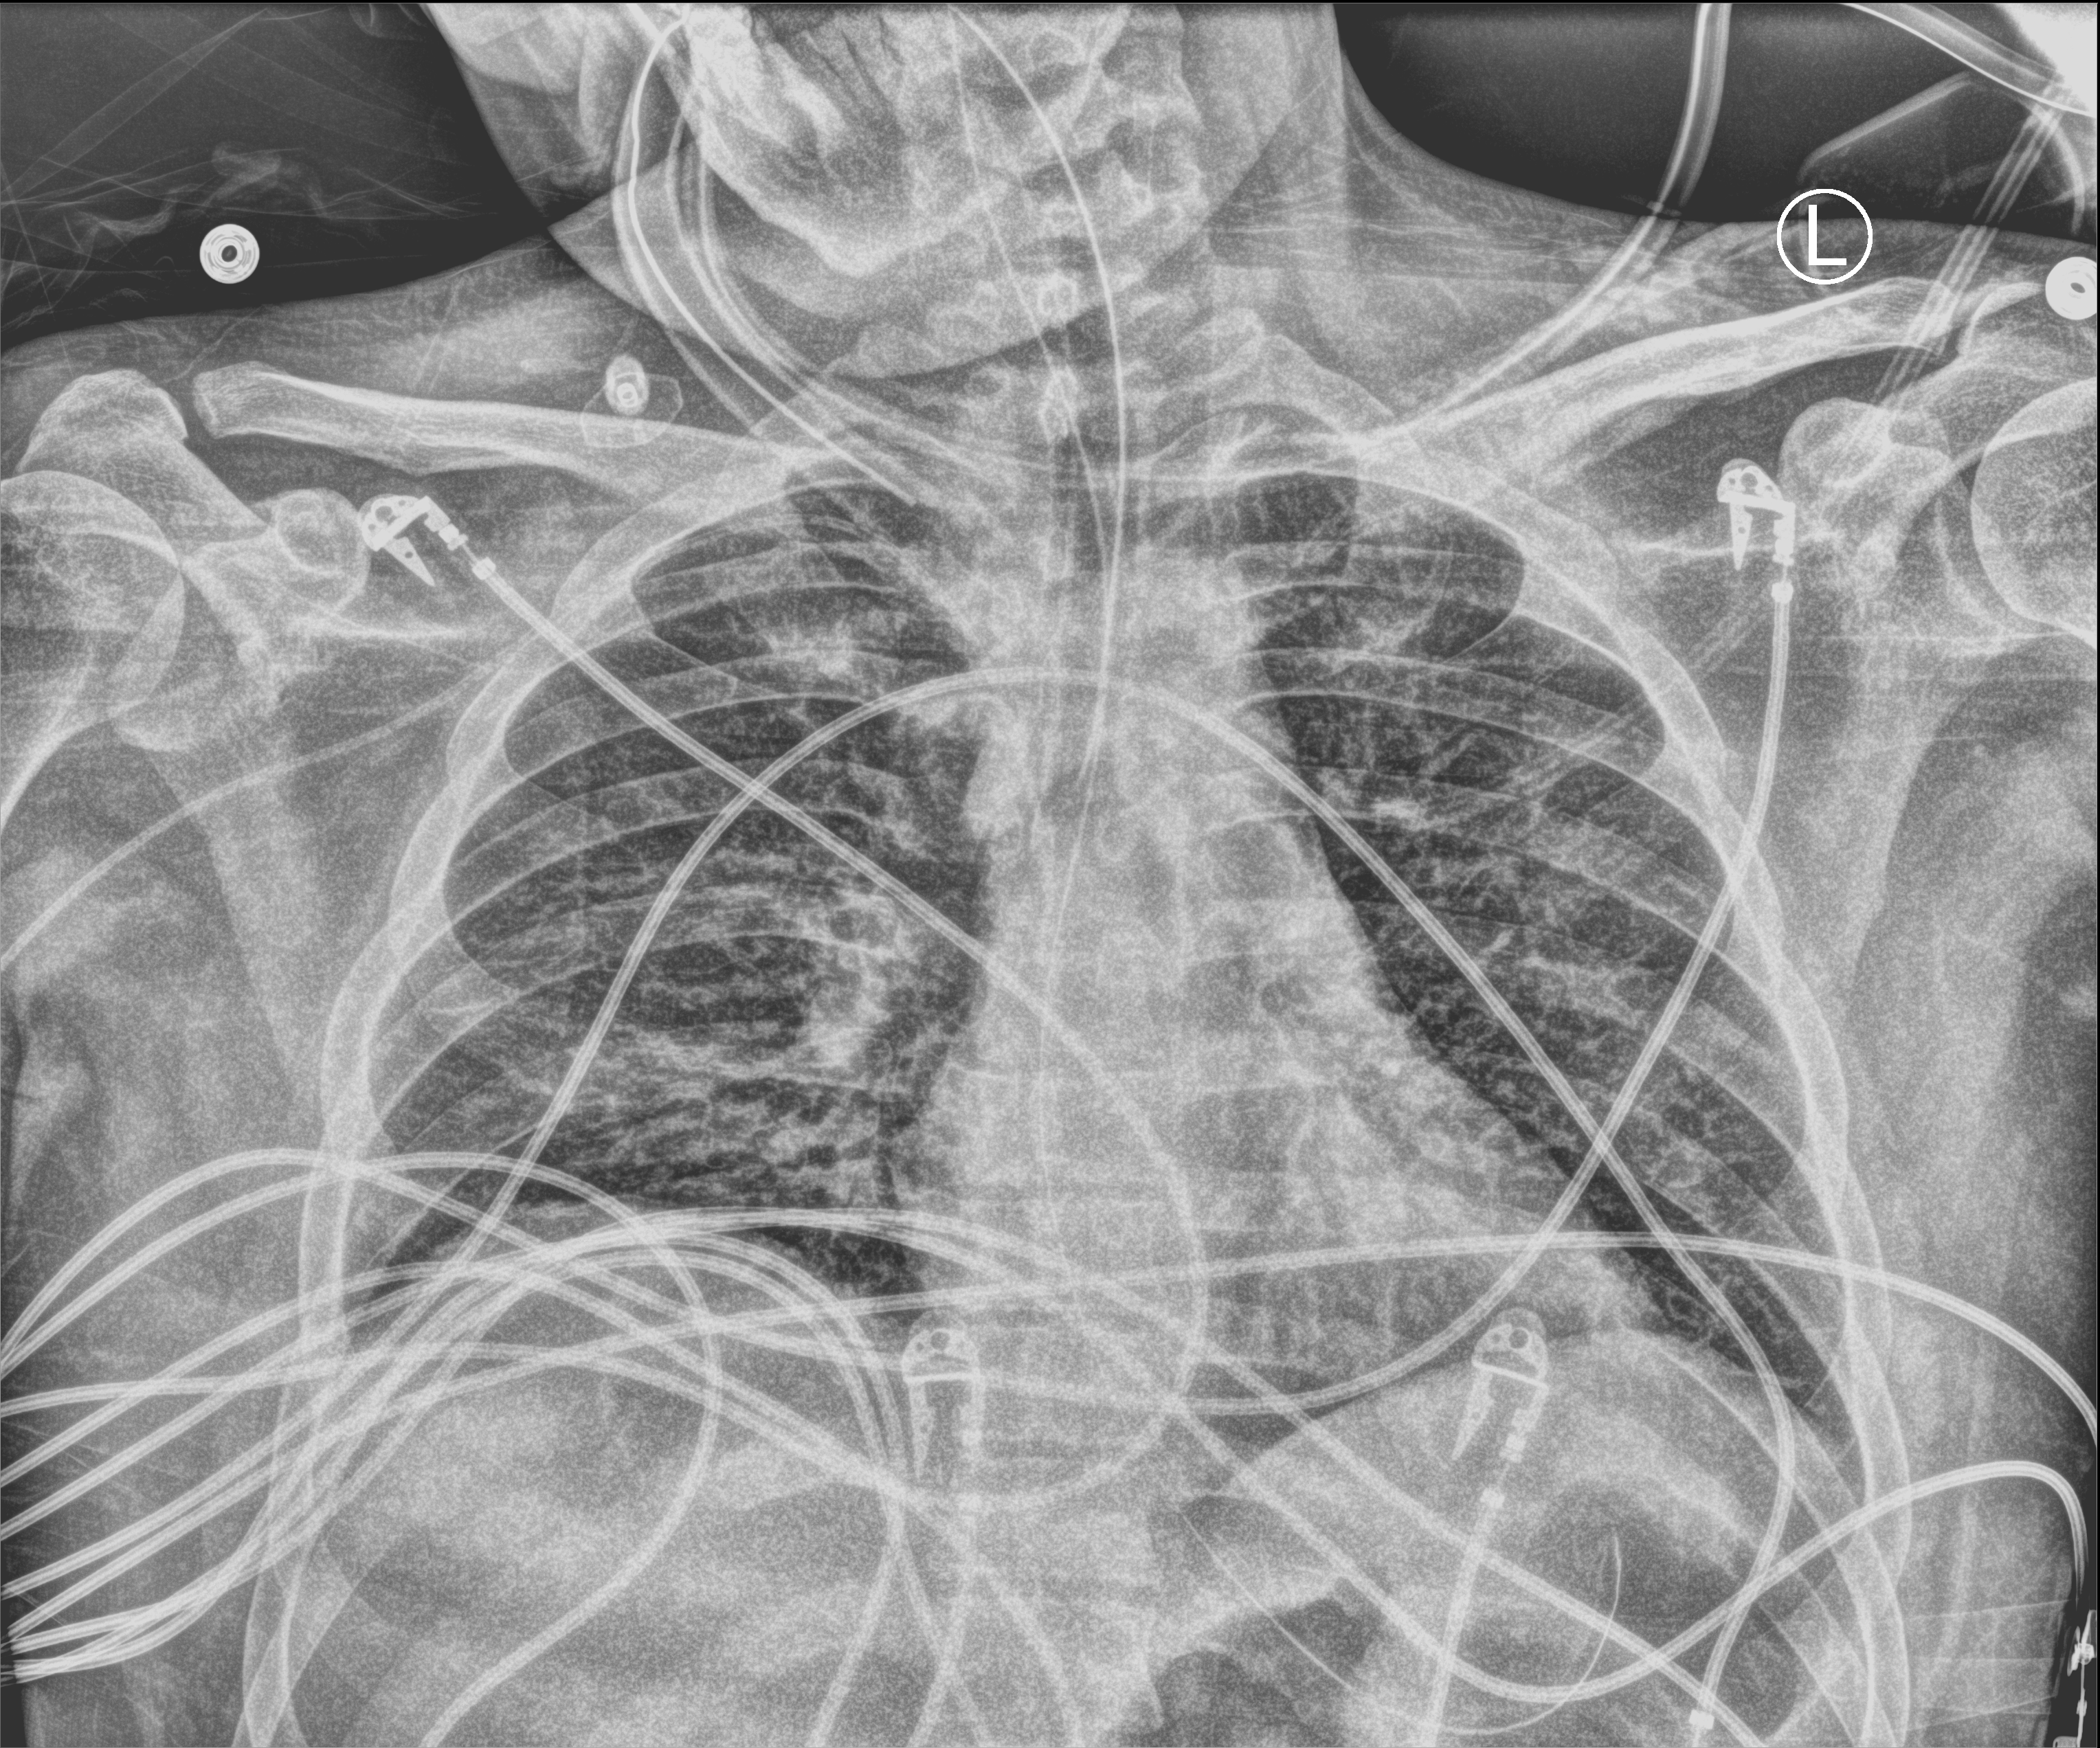
Chest X-ray (portable); anteroposterior (AP) projection. Patient hospitalised with COVID-19; male, aged 18–59 years.
Hospital-stay facts (about this admission, not read from this image; timing relative to this image not recorded):
- other chronic lung disease (admission record): no
- mechanically ventilated during this hospital stay: yes